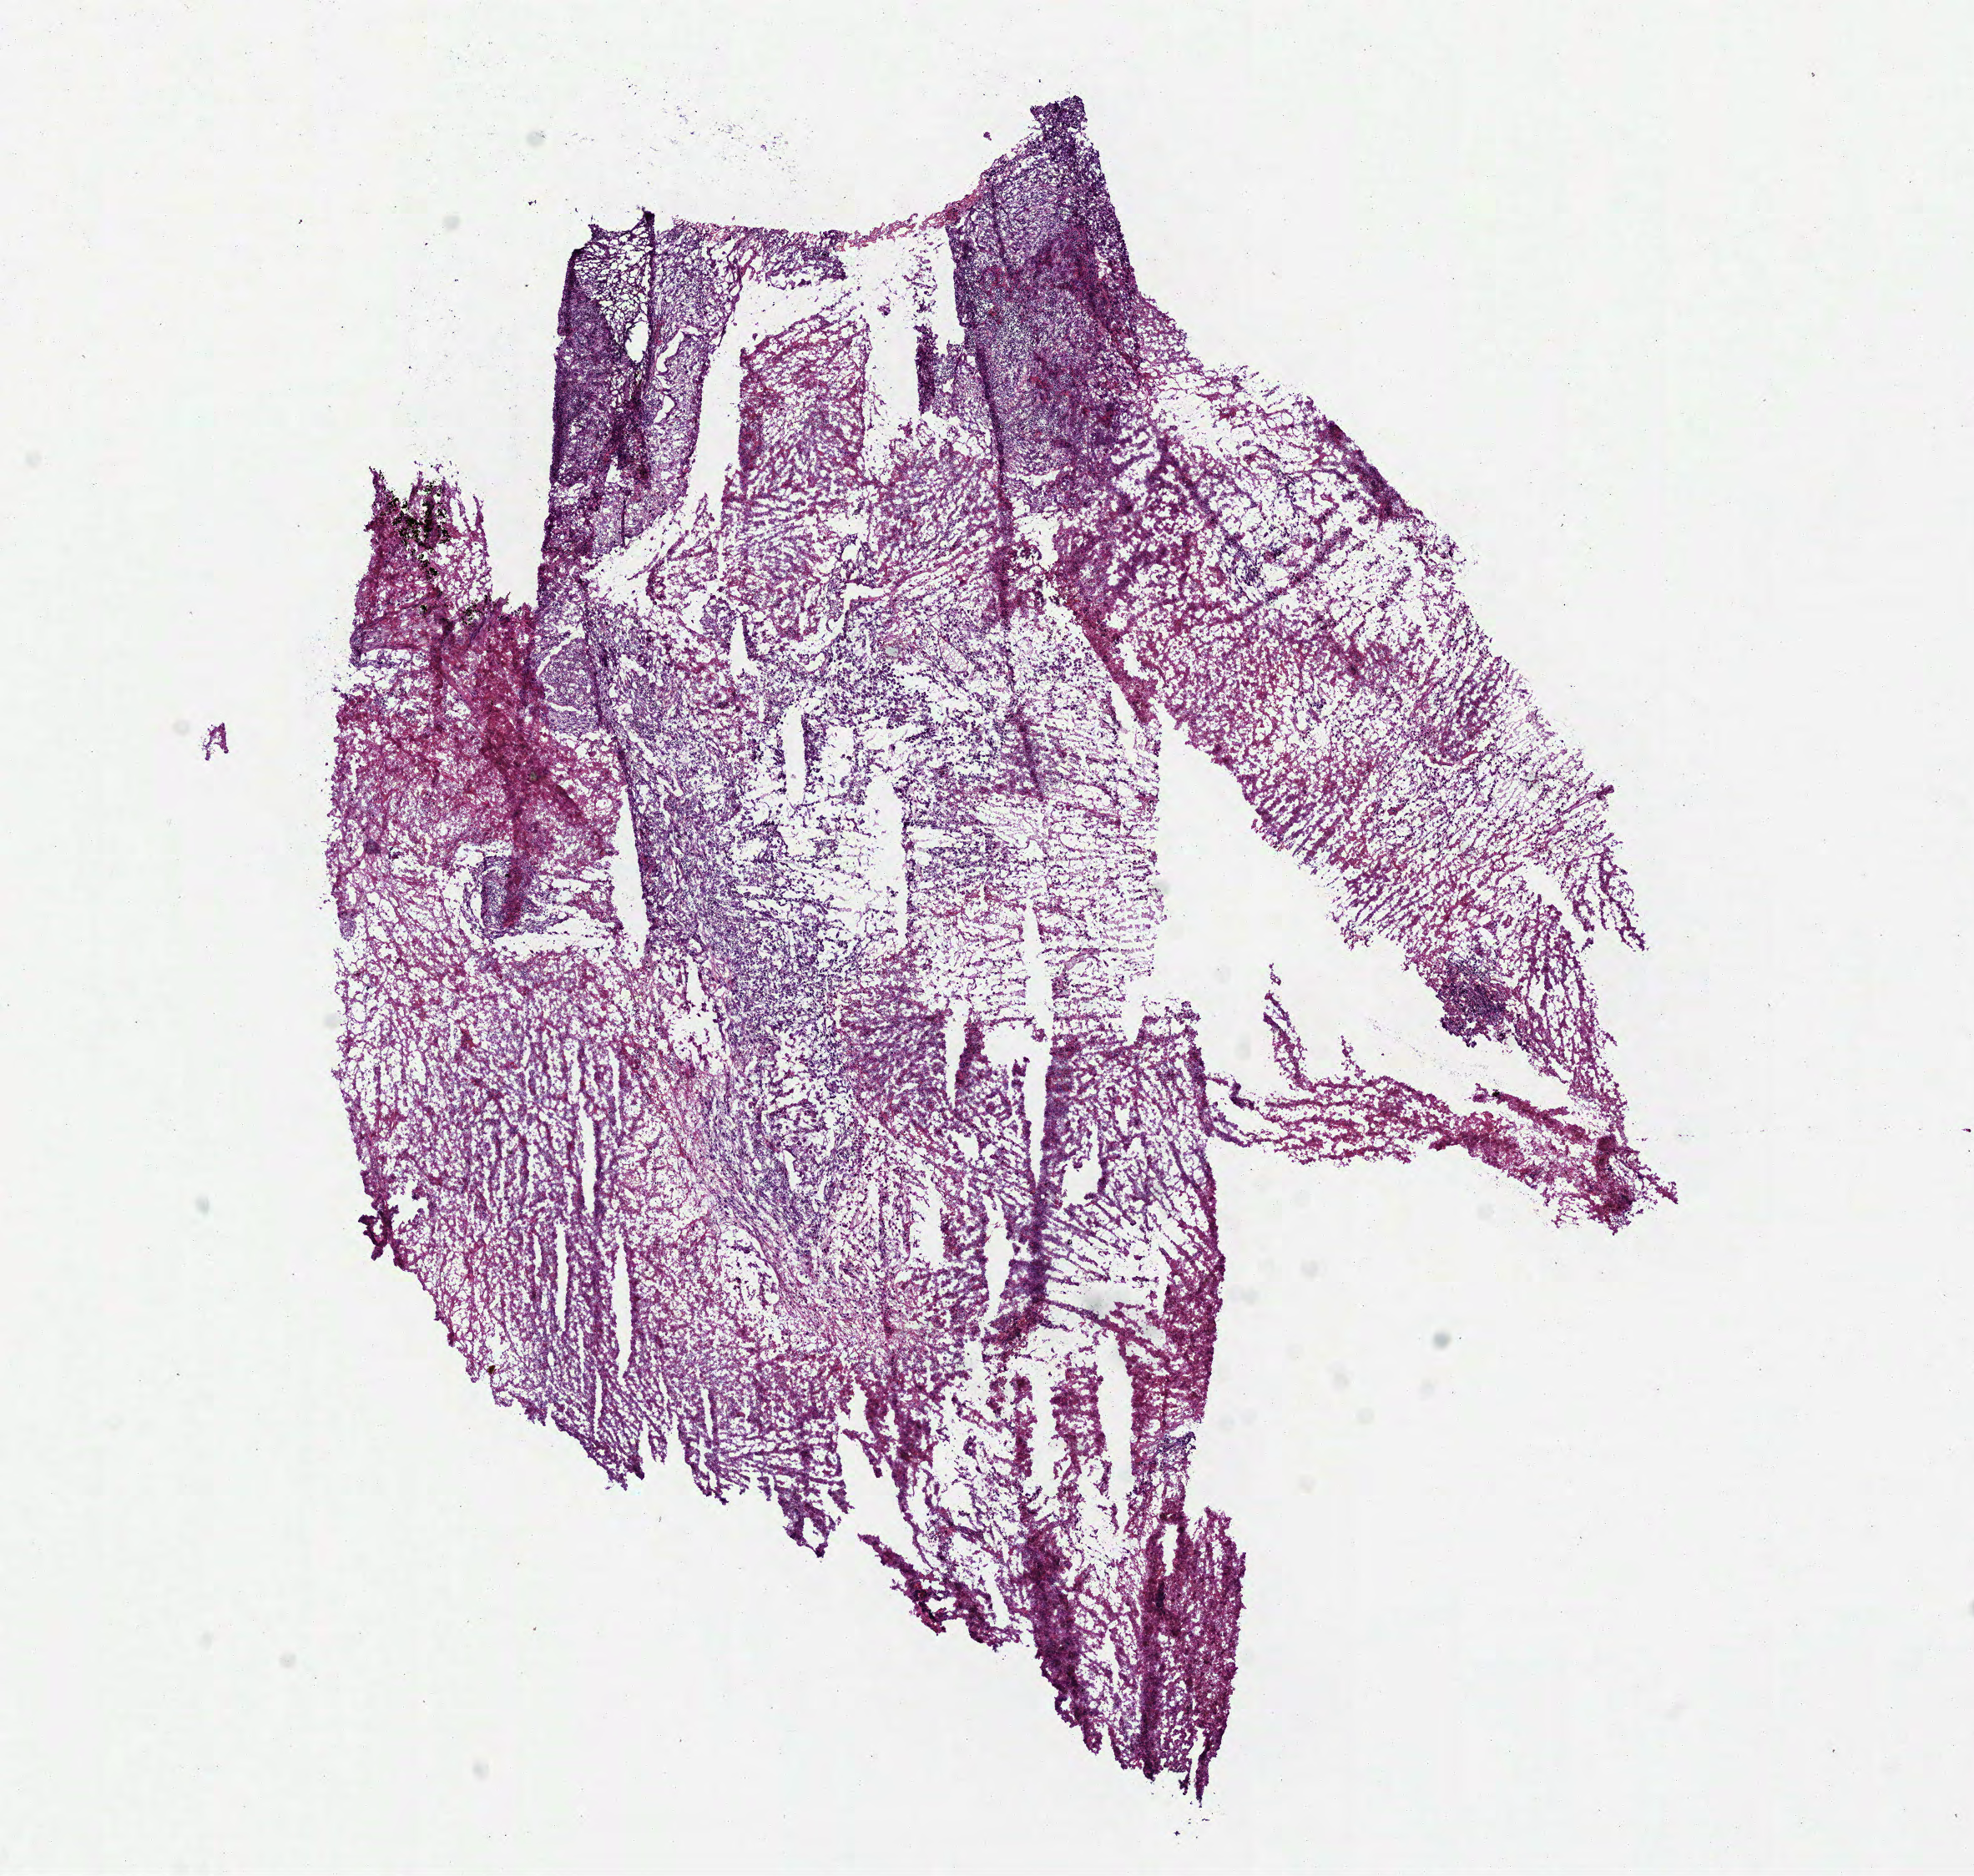
Digitized H&E-stained tissue section (whole slide), low-resolution overview of the scanned area, about 9.5 x 9.1 mm (slide scanned at 40x); frozen section from the bottom of the tissue portion; sample: primary tumour, lung. Male, age 68 years at initial diagnosis. Composition of this section per pathologist review: tumour cells 15%, tumour nuclei 20%, normal cells 0%, stromal cells 5%, necrosis 80%.
TNM: T2 N1 M0. AJCC pathologic stage: IIB (6th edition). Histologic diagnosis: Squamous cell carcinoma, NOS (upper lobe, lung).